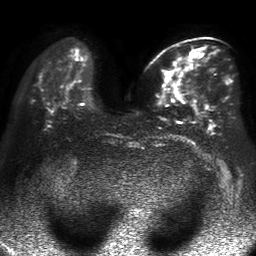
Breast MRI, one axial slice. Slice 18 of 50 in the series (ordered by position). Diffusion-weighted series; image 2 of 4 stored at this slice position (different b-values; order by instance number). 1.5 T. 256 × 256 image matrix, field of view 360 × 360 mm. Female patient.
Structures marked on this image (manually delineated by an expert):
- tumour on diffusion-weighted imaging: bounding box [x1, y1, x2, y2] px = [184, 54, 190, 62]